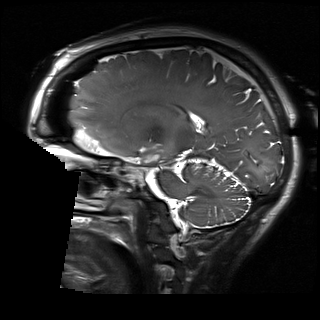
Brain MRI from a brain-tumour surgery series, one sagittal slice. Position 112 of 192 along the scan axis. 320 × 320 image matrix, field of view 230 × 230 mm. Case-level facts recorded for this patient, not image findings: histopathology: Glioblastoma; WHO grade: 2; IDH mutation: no; tumour location: Right Skull Base Temporal.
Outlined on this slice (expert manual segmentation):
- residual tumour: bounding box [x1, y1, x2, y2] px = [146, 155, 159, 162]